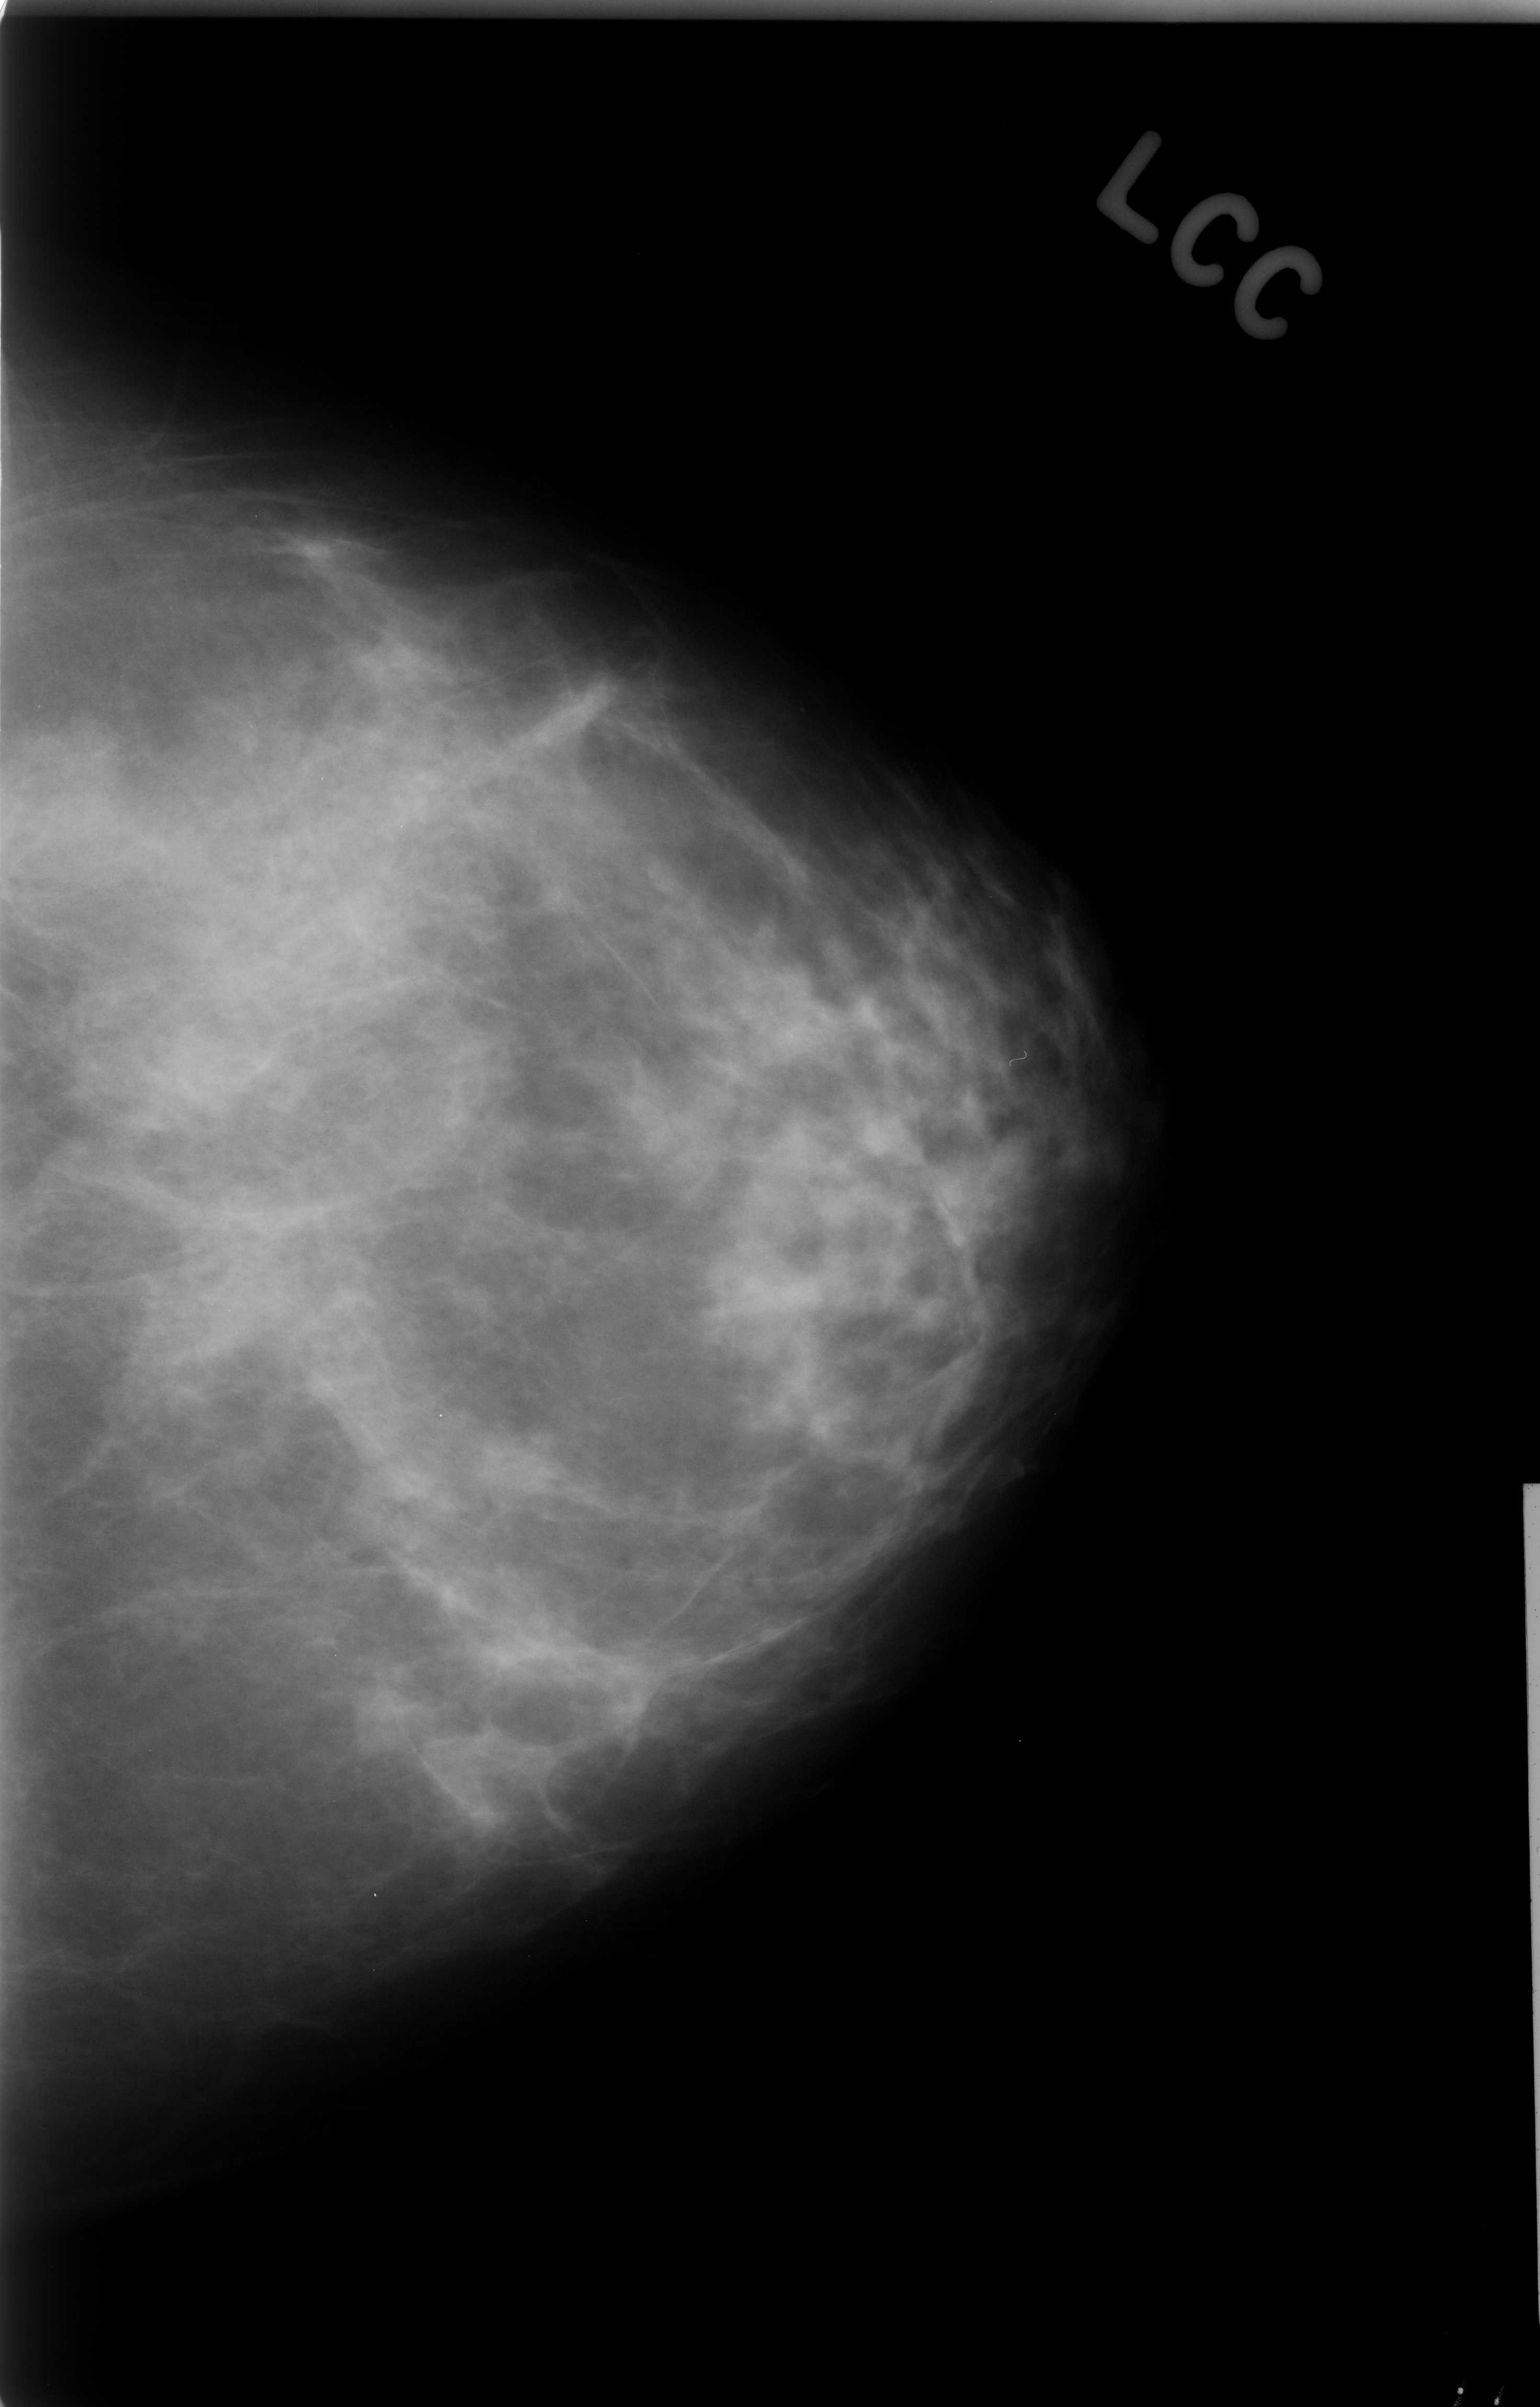
Digitized screen-film mammogram; left breast; craniocaudal (CC) view; BI-RADS breast density category 2 (scale 1–4).
Radiologist-marked abnormalities on this image: mass, shape asymmetric breast tissue; BI-RADS assessment category 3; subtlety rating 5 on a 1 (subtle) to 5 (obvious) scale; benign; no additional work-up was recommended (benign without callback).